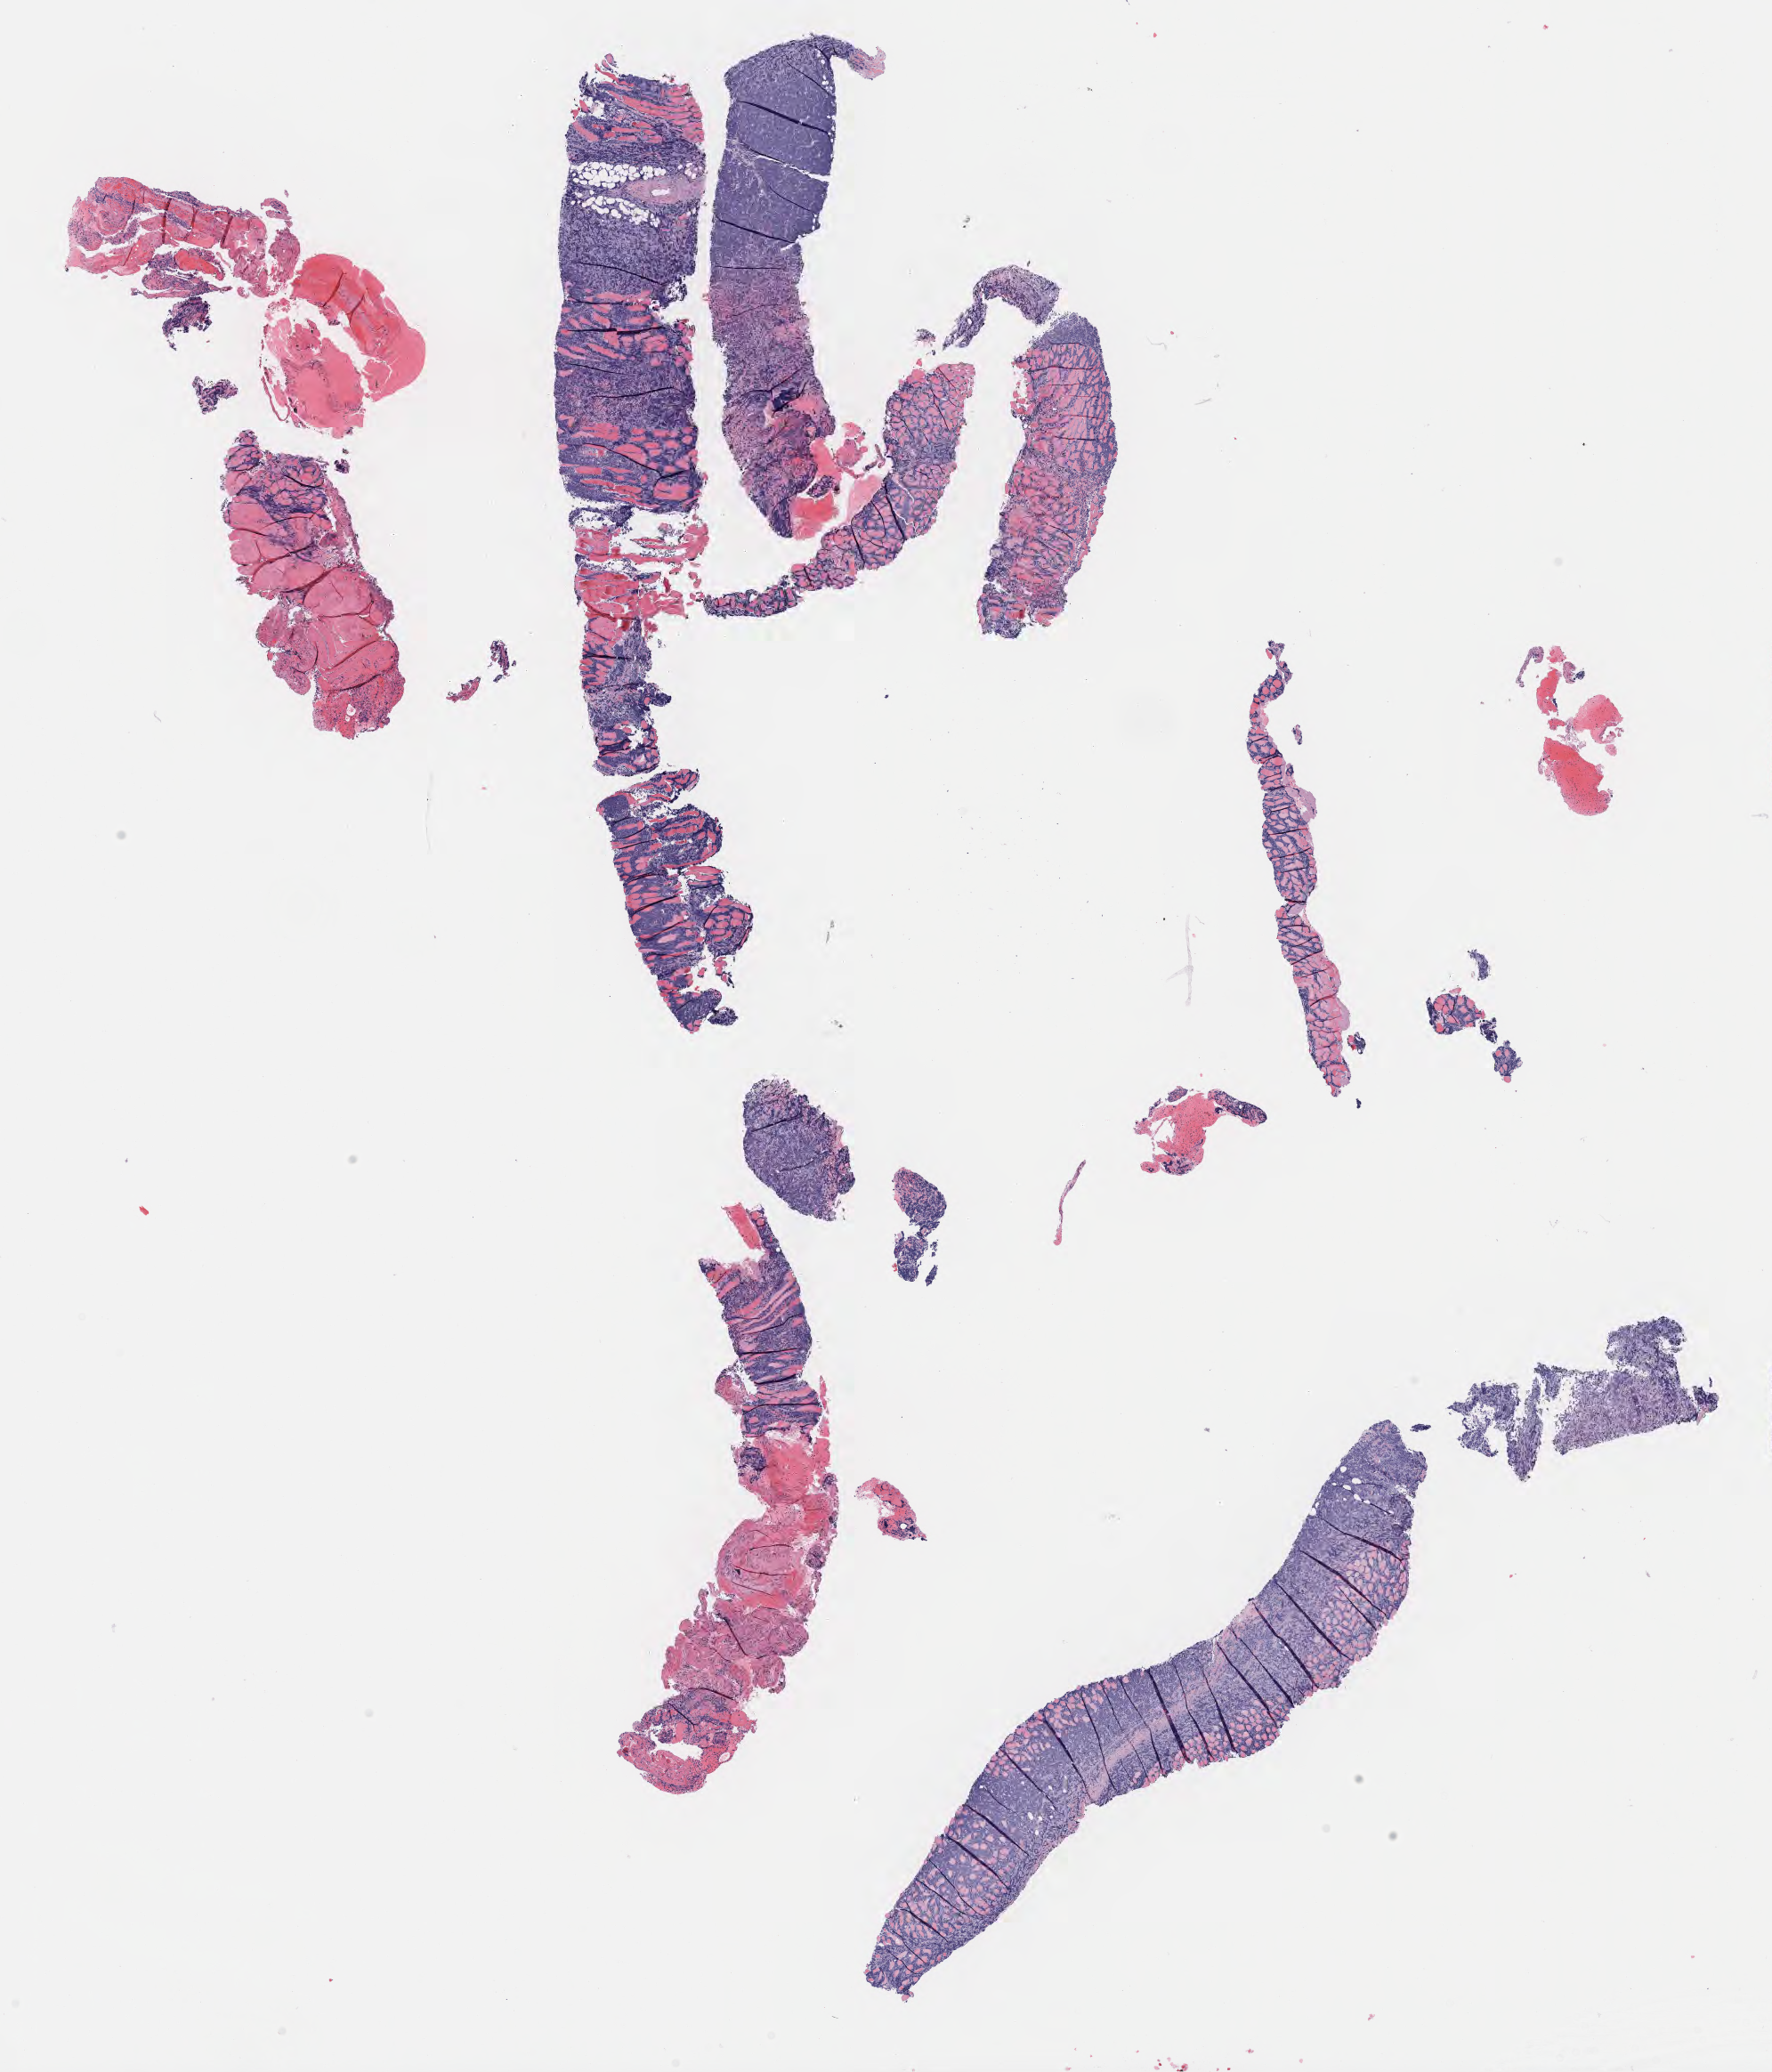
H&E whole-slide image — low-resolution overview of the scanned area, about 16.1 x 18.8 mm, tumor tissue, site: bone of pelvis. Male patient, aged 53.
• diagnosis: Burkitt lymphoma, NOS